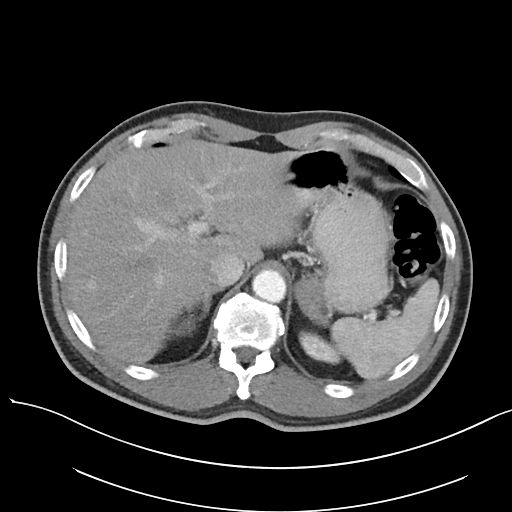
Contrast-enhanced abdominal CT, one axial slice. Slice 82 of 138 in the series (ordered by position). Reconstruction kernel I30f/3. 120 kVp. Intravenous contrast given. Soft-tissue window (W 400 / L 40 HU). 5 mm slice thickness. 512 × 512 image matrix, field of view 400 × 400 mm. Patient: male, 63 years. Case-level facts recorded for this patient, not image findings: diagnosis: adrenocortical carcinoma; tumour side: left adrenal; tumour size at pathology: 4.5 cm.
Structures marked on this image (semi-automatically segmented with operator editing):
- mass: bounding box [x1, y1, x2, y2] px = [294, 278, 330, 327]